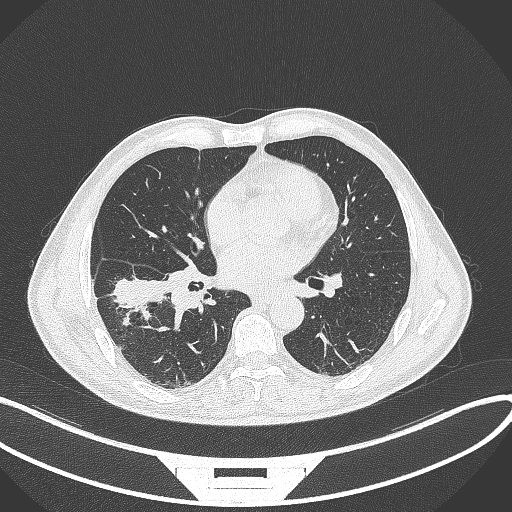
Chest CT, one axial slice. Slice 169 of 364 in the series (ordered by position). 120 kVp. Lung window (W 1500 / L -600 HU). 512 × 512 image matrix, field of view 400 × 400 mm. Patient: male, 58 years. From the clinical record (not read from this slice): clinical TNM (as recorded): T3 N0 M0; histopathological grade: G2.
Structures marked on this image (bounding box drawn by a radiologist):
- lung tumour (recorded histology: squamous cell carcinoma): bounding box (x1, y1, x2, y2) in pixels: (114, 276, 168, 311)